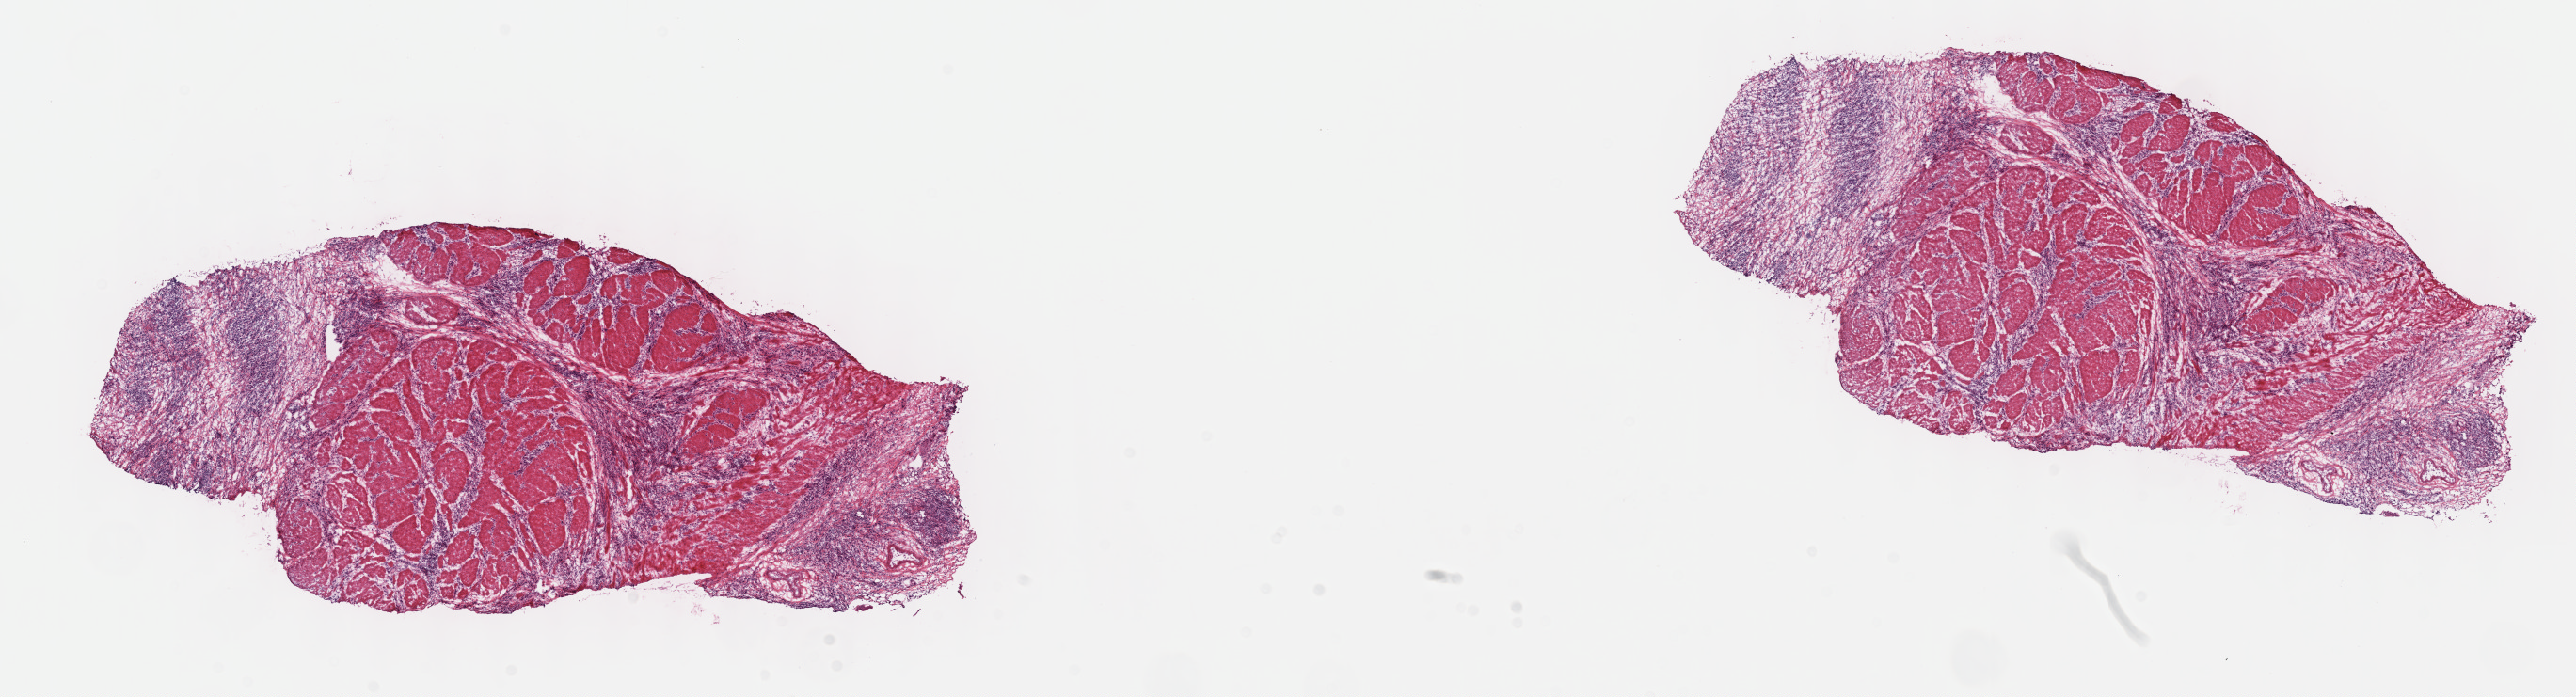
Whole-slide histology image, H&E — a low-resolution overview of the entire scanned area, about 22.1 x 6.0 mm. Frozen section from the top of the tissue portion. Primary tumour sample from the stomach. Female, age 52 years at initial diagnosis. Histologic grade: G3 (poorly differentiated). Pathologist review of this section (percent, as recorded): tumour cells 30%, tumour nuclei 40%, normal cells 40%, stromal cells 30%, necrosis 0%. Infiltration values recorded for this section: lymphocyte infiltration 0%, monocyte infiltration 0%, neutrophil infiltration 0%.
AJCC pathologic stage: IIIB (7th edition). Pathologic diagnosis: Carcinoma, diffuse type. Lymph nodes positive (case pathology): 13 of 22 examined.